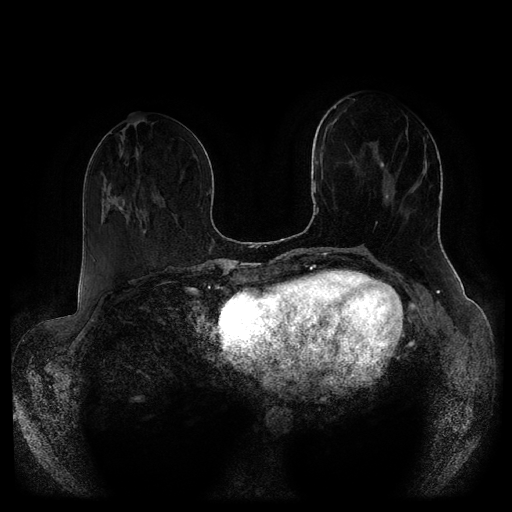
Breast MRI (dynamic contrast-enhanced, multi-phase), one axial slice. Slice 36 of 116 in the series (ordered by position). Dynamic contrast-enhanced series, time point 2 of 5 at this slice position (early post-contrast). 1.5 T. TE 2.6 ms, TR 5.3 ms. 2 mm slice thickness. 512 × 512 image matrix. Female patient, age 51 years.
Outlined on this slice (semi-automatic segmentation, software-assisted and operator-edited):
- breast lesion (labelled 'tumour' in the annotation; benign lesions carry a separate 'benign' label): box from (x=380, y=162) to (x=384, y=167) px